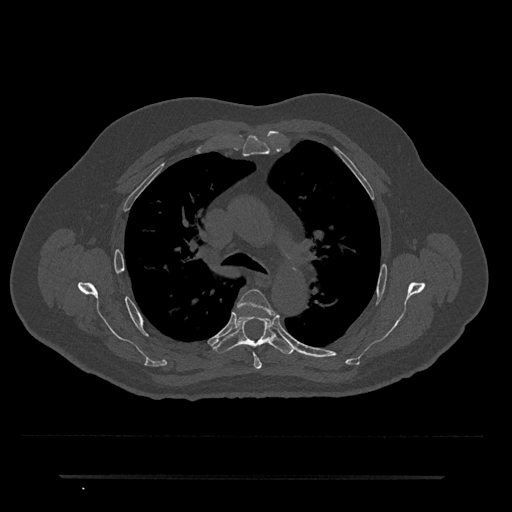
CT including the spine, one axial slice. Slice 500 of 797 in the series (ordered by position). Reconstruction kernel Br40s/3. 120 kVp. Bone window (W 1800 / L 400 HU). 0.5 mm slice thickness. 512 × 512 image matrix. Male patient, age 69 years. Case-level facts recorded for this patient, not image findings: primary cancer: prostate.
Annotated regions visible in this slice (semi-automatically segmented with operator editing):
- T4 vertebra: bounding box (x1, y1, x2, y2) in pixels: (238, 289, 276, 369)
- T5 vertebra: (212, 316, 296, 355)